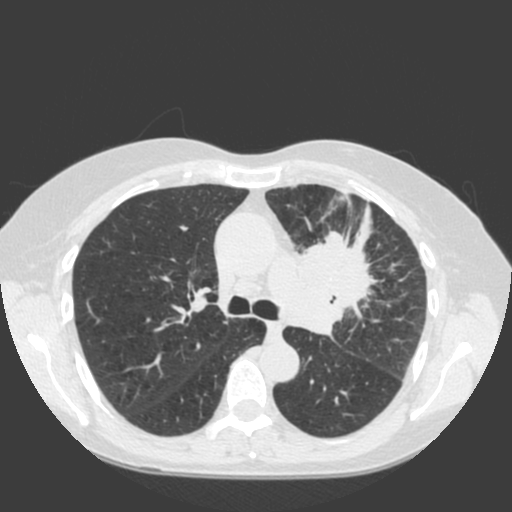
Low-dose screening chest CT, one axial slice; position 124 of 184 along the scan axis; 120 kVp; lung window (W 1500 / L -600 HU); 2 mm slice thickness; 512 × 512 image matrix.
Outlined on this slice (outlined manually by an expert reader):
- lesion 1 (tumor, hilum of left lung): bounding box (x1, y1, x2, y2) in pixels: (288, 208, 377, 335)